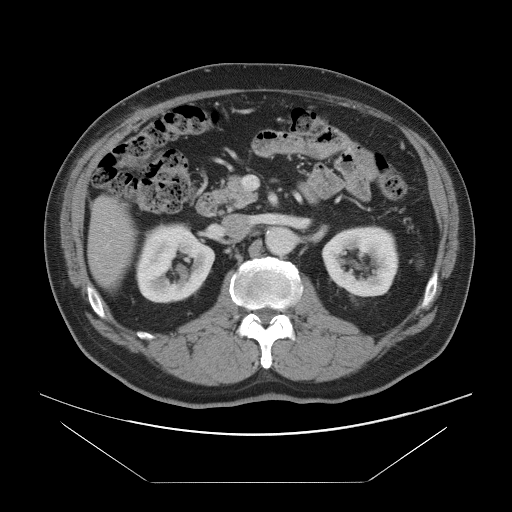
Contrast-enhanced abdominal CT, one axial slice. Slice 40 of 97 in the series (ordered by position). 120 kVp. Intravenous contrast given. Soft-tissue window (W 400 / L 40 HU). 5 mm slice thickness. 512 × 512 image matrix. Male patient, age 62 years. Case-level facts recorded for this patient, not image findings: diagnosis: colorectal cancer liver metastases, imaged before liver resection; multiple liver metastases: no; largest metastasis: 7 cm; disease in both lobes: yes.
Annotated regions visible in this slice (outlined manually by an expert reader):
- hepatic veins: bounding box <104,228,108,232> (left, top, right, bottom; pixels)
- liver: <90,198,133,287>
- planned liver remnant (the part of the liver to remain after resection): <90,198,133,286>